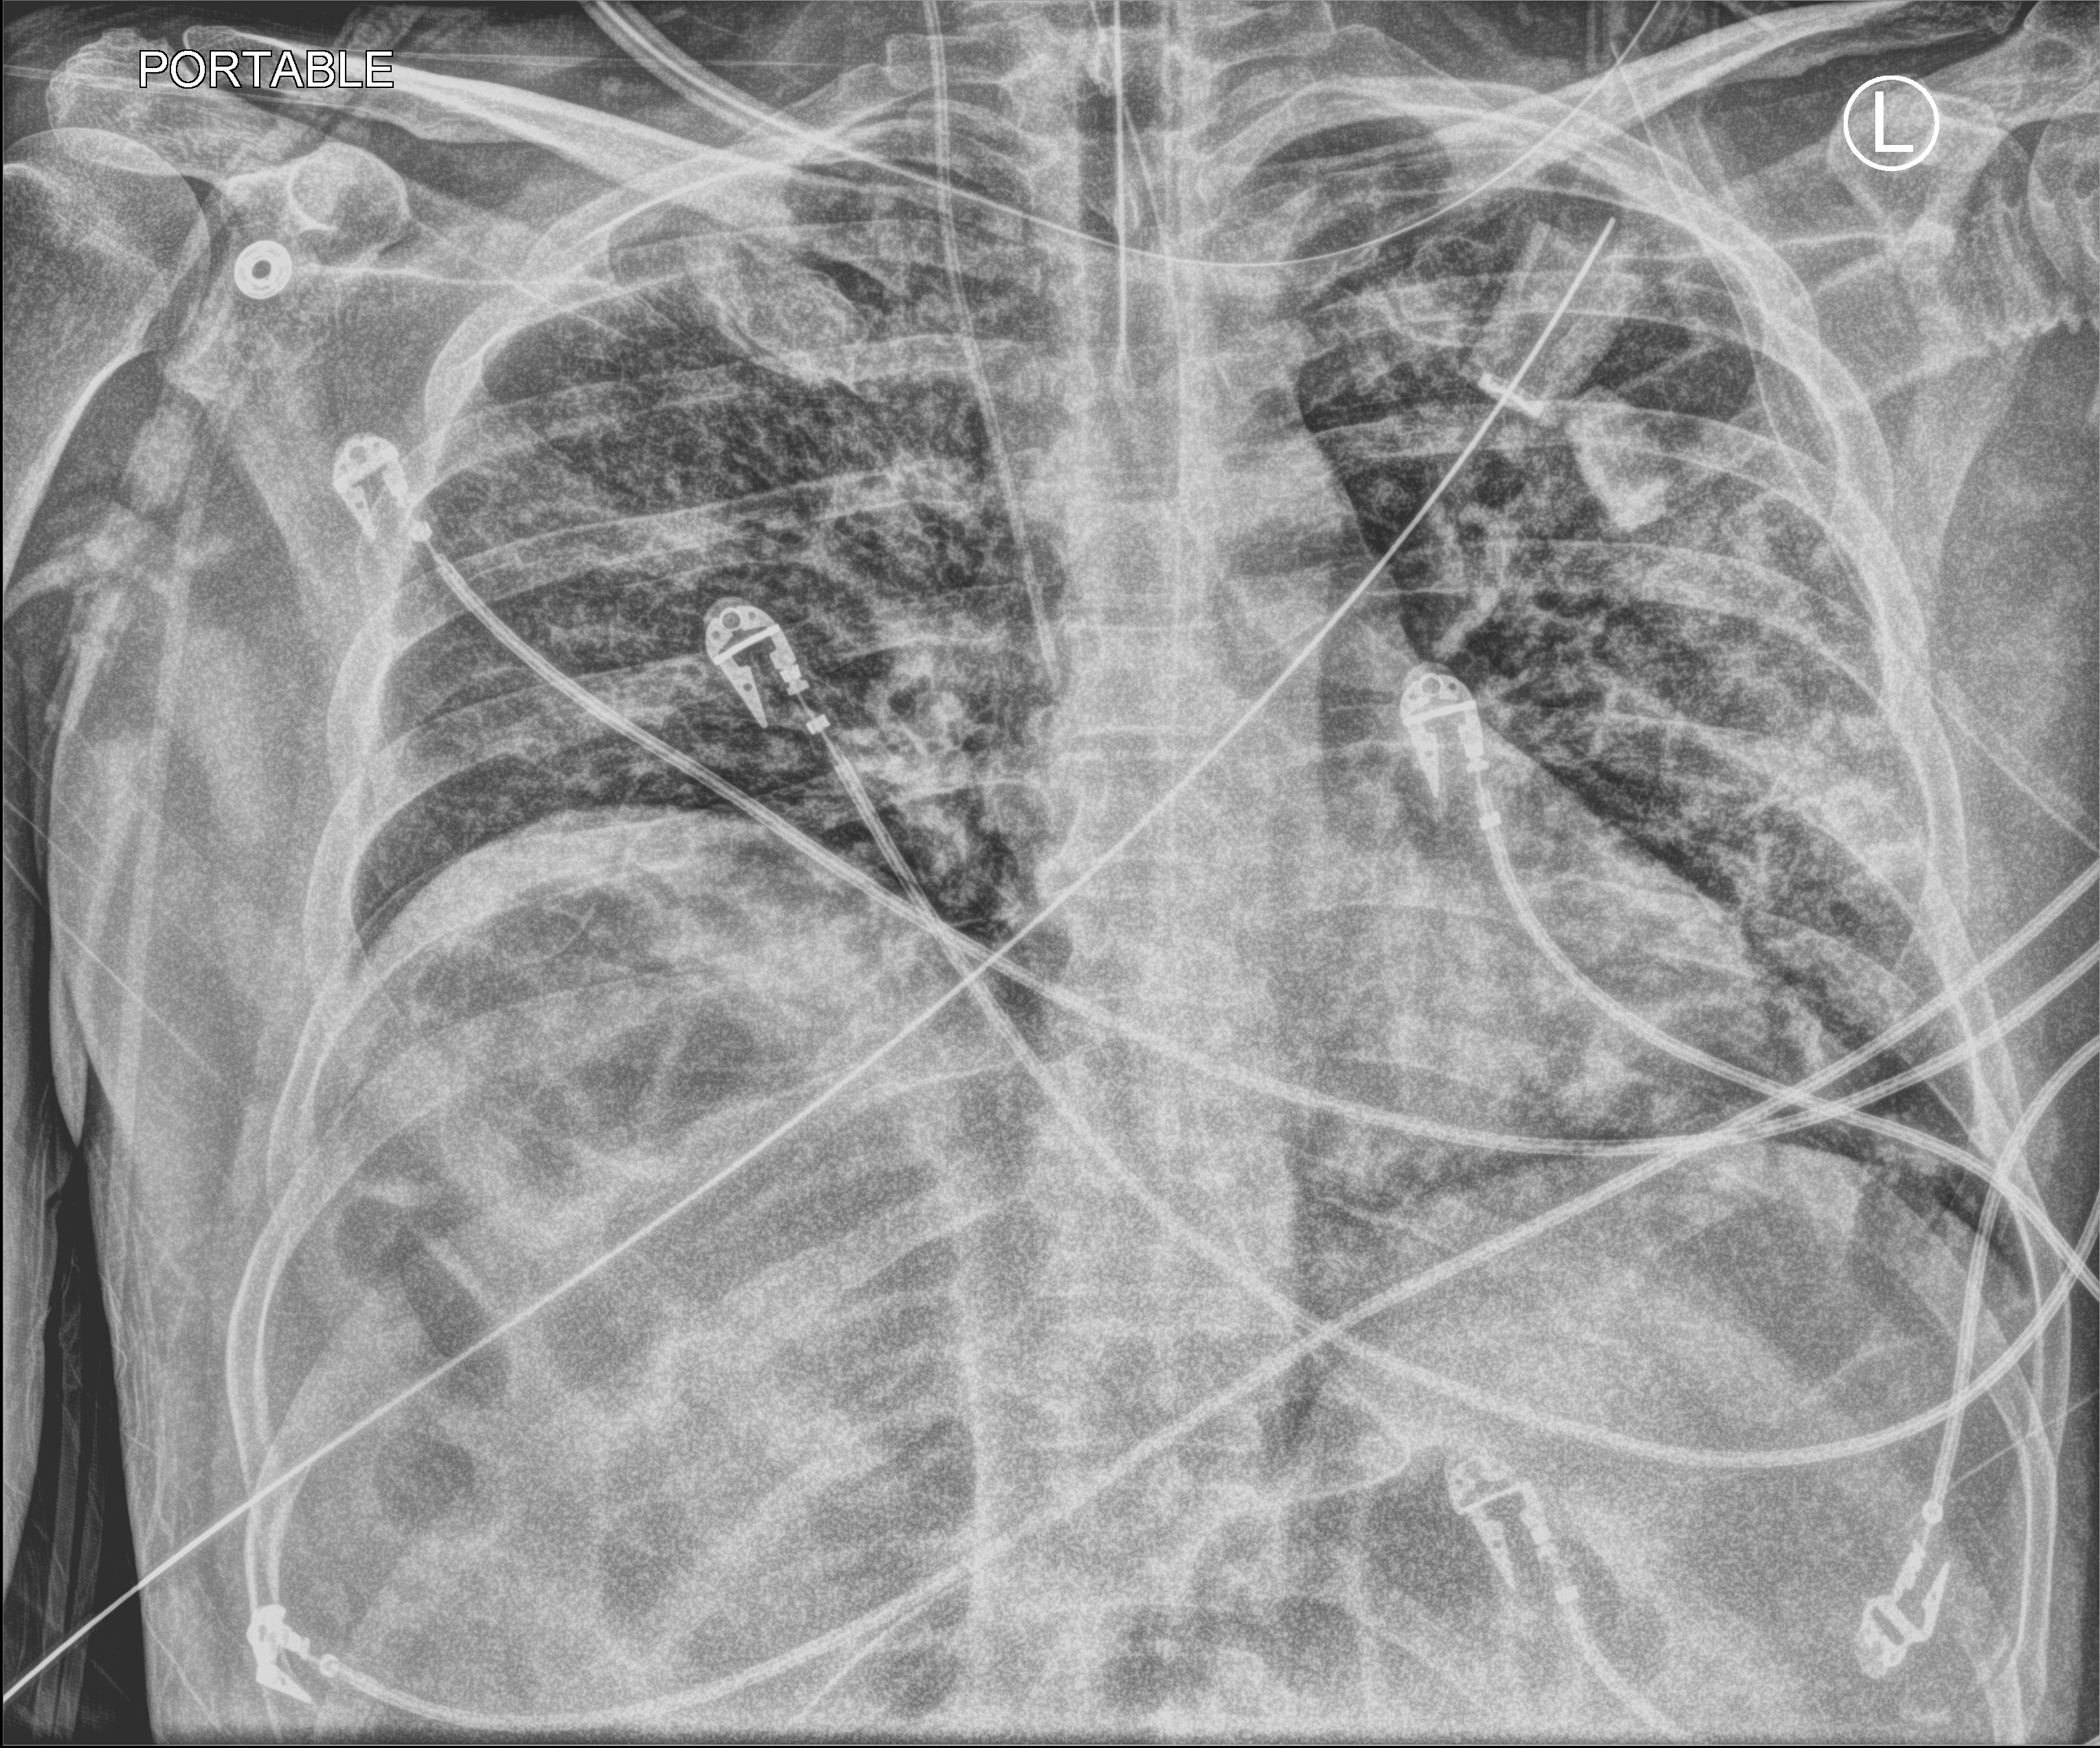
Chest X-ray (portable); anteroposterior (AP) projection. Patient hospitalised with COVID-19; male, aged 18–59 years.
Hospital-stay facts (about this admission, not read from this image; timing relative to this image not recorded): admitted to intensive care during this hospital stay: yes; smoking status (admission record): never; mechanically ventilated during this hospital stay: yes.